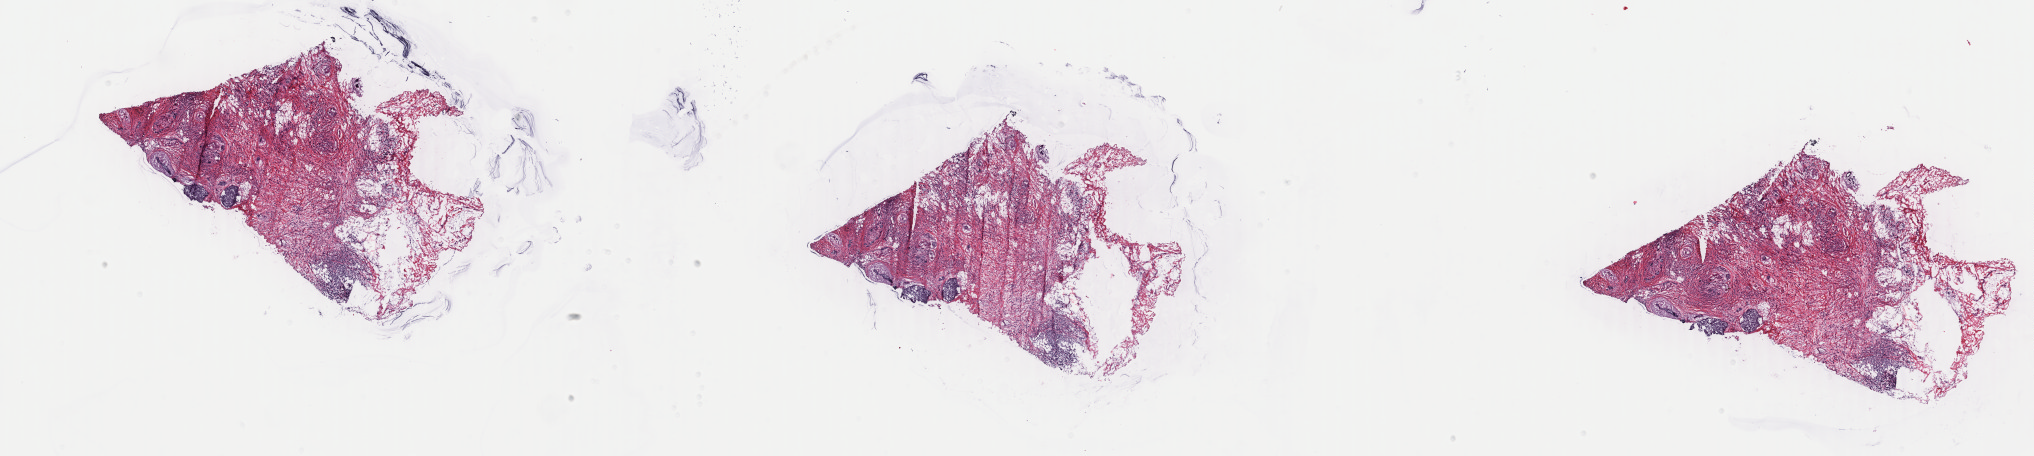
H&E-stained whole-slide image, shown as a low-resolution overview of the whole scanned area (about 32.4 x 7.3 mm), frozen section from the top of the tissue portion, primary tumour sample from the breast. Patient: female, age at initial diagnosis 55 years. Composition of this section per pathologist review: tumour cells 85%, tumour nuclei 85%, normal cells 5%, stromal cells 10%, necrosis 0%. Infiltration values recorded for this section: lymphocyte infiltration 0%, monocyte infiltration 0%, neutrophil infiltration 0%.
• AJCC pathologic stage: IA
• histologic diagnosis: Infiltrating duct carcinoma, NOS
• laterality: right